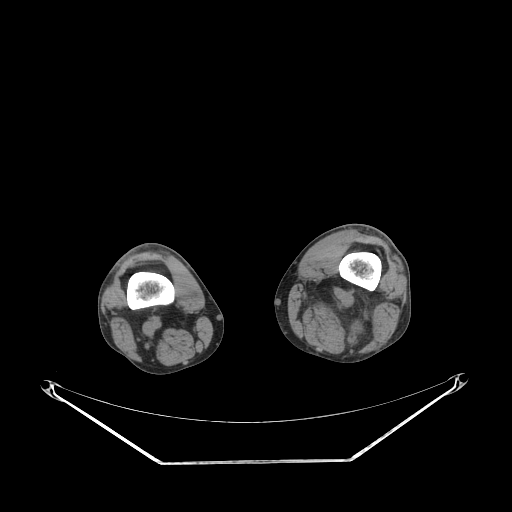
CT of an extremity soft-tissue mass (from a PET/CT study), one axial slice; position 200 of 267 along the scan axis; reconstruction kernel STANDARD; 140 kVp; soft-tissue window (W 400 / L 40 HU); 512 × 512 image matrix, field of view 500 × 500 mm. Male patient. Case-level facts recorded for this patient, not image findings: histological type: undifferentiated pleomorphic liposarcoma; grade: high; site of the primary tumour: left thigh.
Outlined on this slice (expert contour drawn on MRI and transferred to this co-registered scan by the dataset authors):
- gross tumour volume including surrounding oedema: bounding box <297,279,380,325> (left, top, right, bottom; pixels)